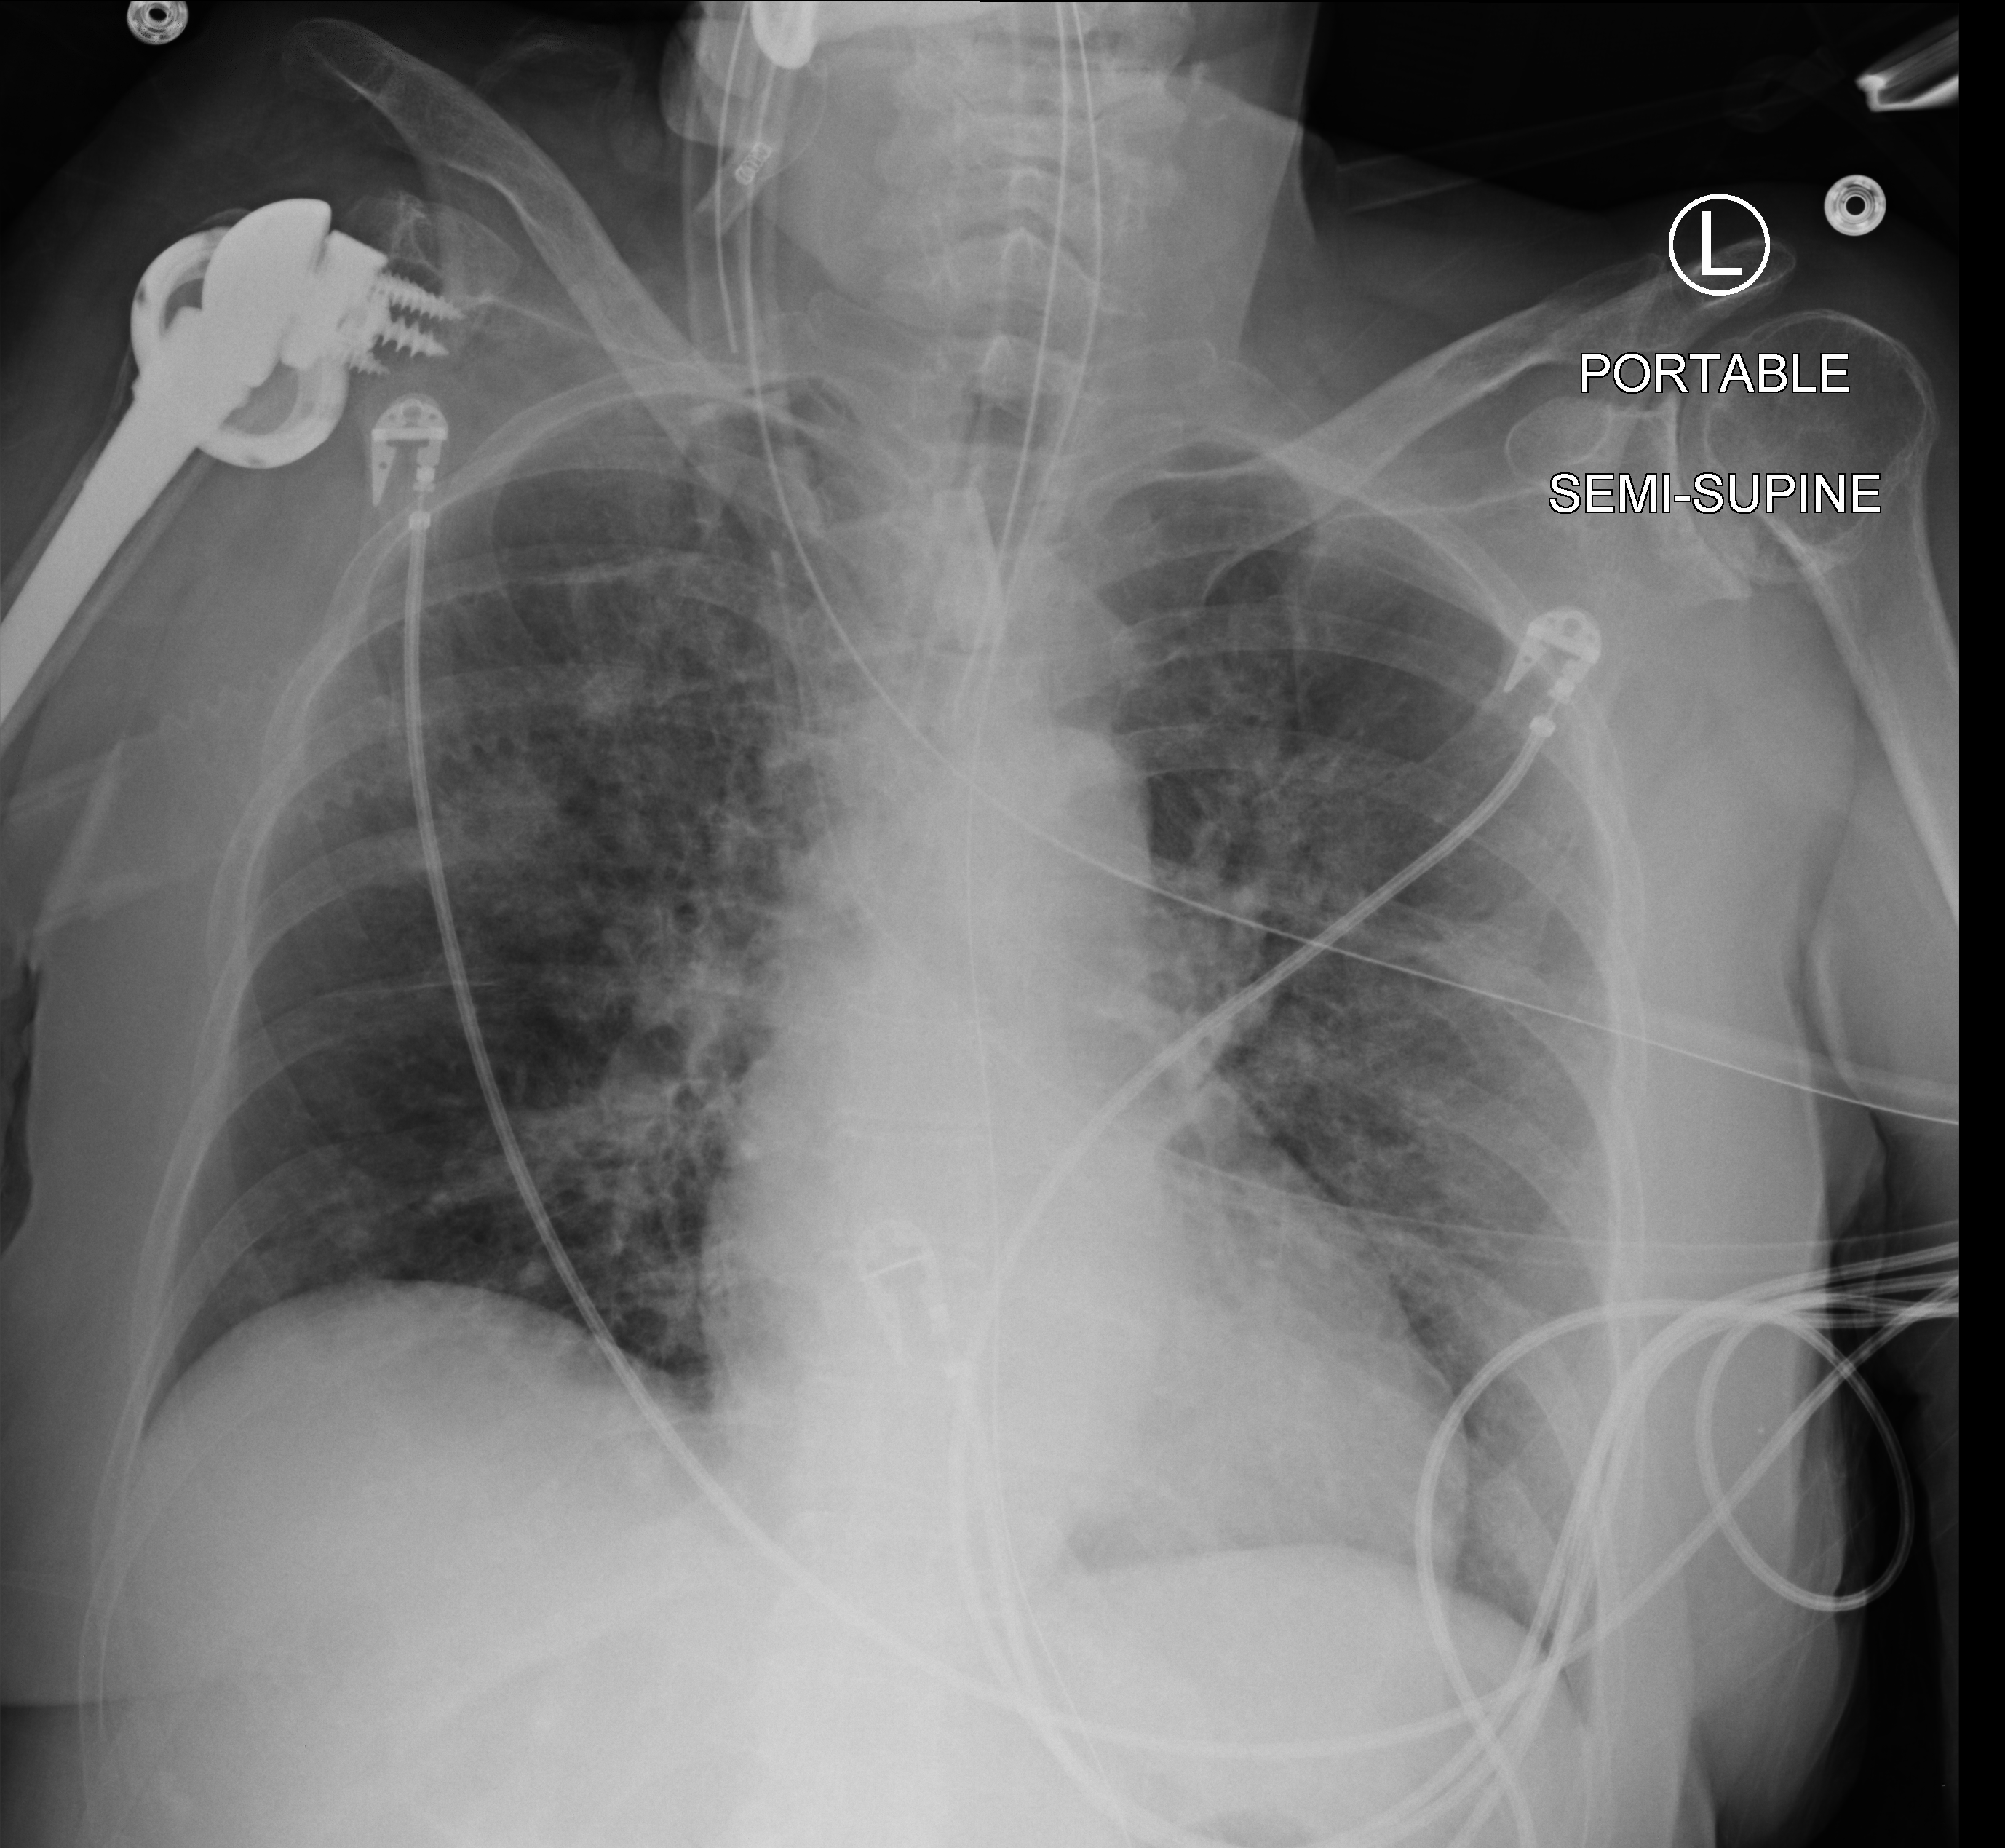
Bedside chest radiograph (computed radiography), anteroposterior (AP) projection. Patient hospitalised with COVID-19; female, aged 60–74 years.
Hospital-stay facts (about this admission, not read from this image; timing relative to this image not recorded): admitted to intensive care during this hospital stay: yes.